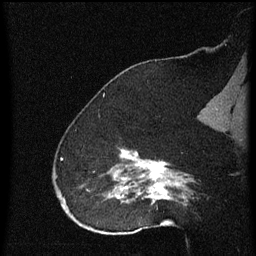
Breast MRI (dynamic contrast-enhanced), one sagittal slice; slice 42 of 60 in the series (ordered by position); dynamic contrast-enhanced series, image 2 of 4 at this slice position (ordered by acquisition); 1.5 T; TE 4.2 ms, TR 8 ms; 256 × 256 image matrix, field of view 180 × 180 mm. Female patient, age 52 years.
Outlined on this slice (semi-automatic segmentation, software-assisted and operator-edited):
- analysis volume of interest (the breast-tissue region the enhancement analysis was run in; not a lesion): bounding box (x1, y1, x2, y2) in pixels: (73, 148, 172, 219)
- tumour enhancement mask (voxels above the 70 % enhancement threshold inside the analysis volume of interest): (109, 150, 172, 203)